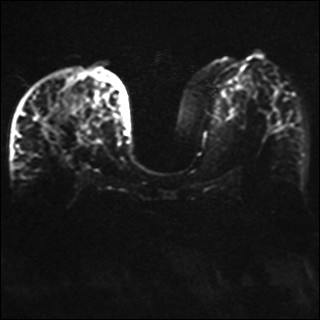
Breast MRI, one axial slice. Position 17 of 42 along the scan axis. Diffusion-weighted series; image 2 of 4 stored at this slice position (different b-values; order by instance number). 1.5 T. 4 mm slice thickness. 320 × 320 image matrix, field of view 330 × 330 mm. Female patient.
Outlined on this slice (outlined manually by an expert reader):
- tumour on diffusion-weighted imaging: box from (x=33, y=115) to (x=47, y=136) px